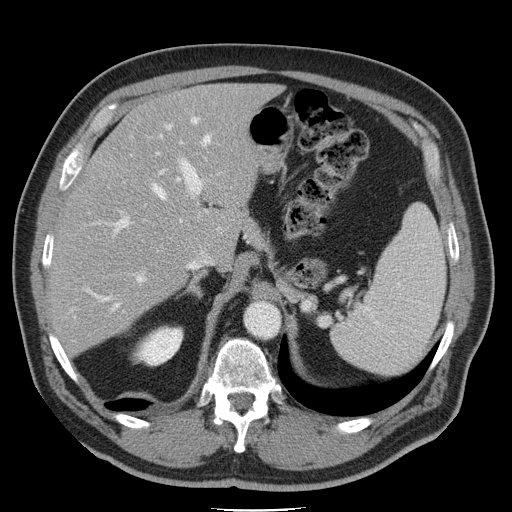
Contrast-enhanced abdominal CT, one axial slice; slice 31 of 45 in the series (ordered by position); 120 kVp; intravenous contrast given; soft-tissue window (W 400 / L 40 HU); 5 mm slice thickness; 512 × 512 image matrix, field of view 386 × 386 mm. Male patient, age 65 years. From the clinical record (not read from this slice): diagnosis: colorectal cancer liver metastases, imaged before liver resection; multiple liver metastases: yes; largest metastasis: 4.9 cm; disease in both lobes: no.
Structures marked on this image (expert manual segmentation):
- hepatic veins: bounding box [x1, y1, x2, y2] px = [82, 123, 213, 336]
- liver: [53, 84, 274, 350]
- planned liver remnant (the part of the liver to remain after resection): [102, 84, 274, 257]
- portal vein (with intrahepatic branches): [90, 117, 203, 286]